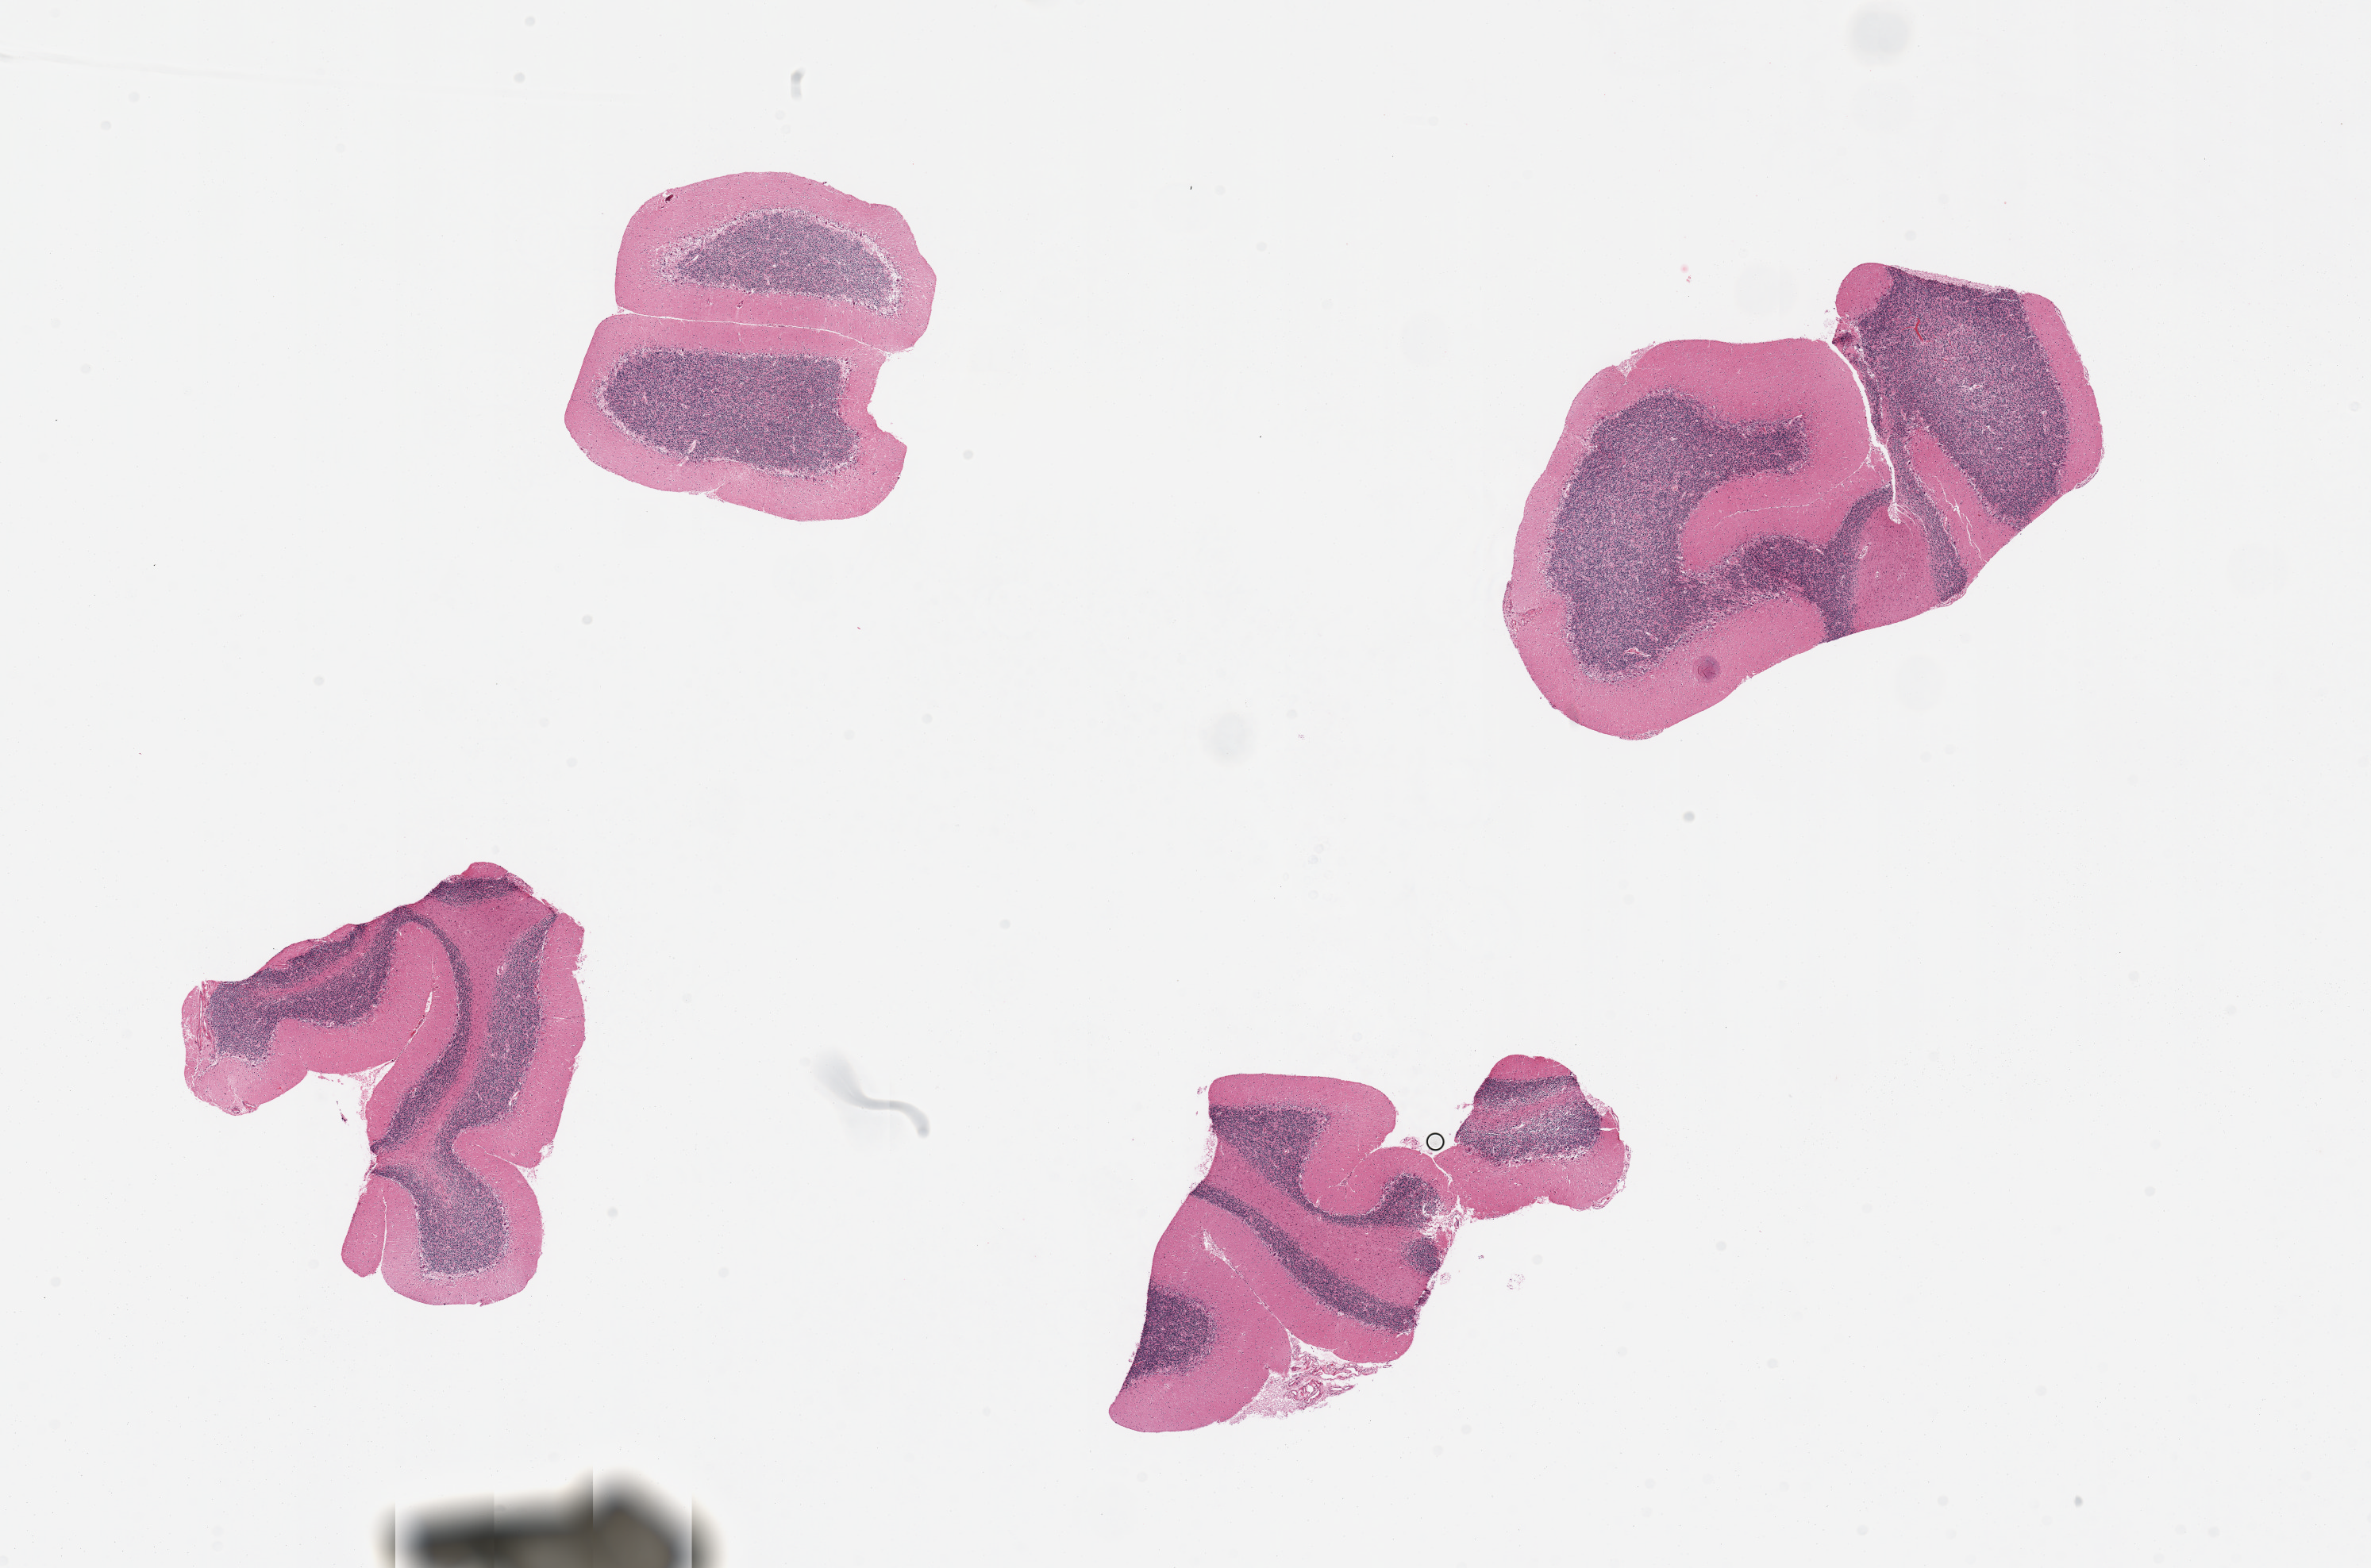
Digitized H&E-stained section, low-resolution overview of the scanned area, about 23.6 x 15.6 mm, PAXgene-fixed, paraffin-embedded tissue, section of cerebellum (target tissue), donor tissue sample.
Reviewer comment on this tissue sample: 4 pieces.